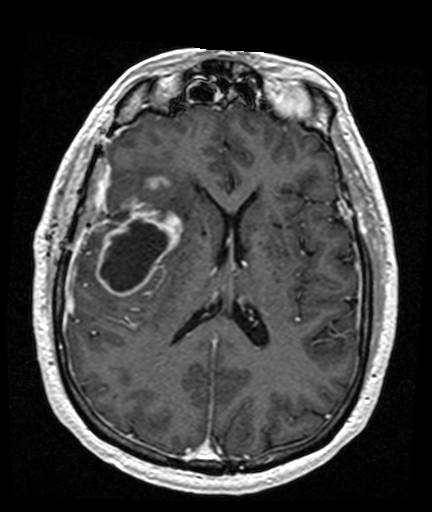
Brain MRI from a brain-tumour surgery series, one axial slice; position 73 of 176 along the scan axis; T1-weighted post-contrast; 1 mm slice thickness; 432 × 512 image matrix, field of view 194 × 230 mm. Case-level facts recorded for this patient, not image findings: histopathology: Glioblastoma; WHO grade: 4; IDH mutation: no.
Structures marked on this image (outlined manually by an expert reader):
- tumour: bounding box (x1, y1, x2, y2) in pixels: (96, 176, 182, 297)